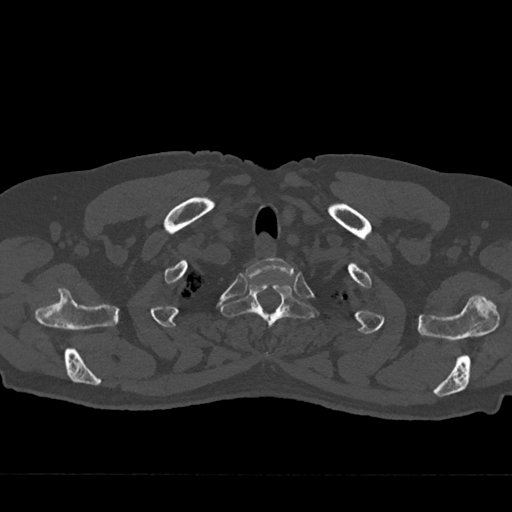
CT including the spine, one axial slice; slice 625 of 797 in the series (ordered by position); reconstruction kernel Br40s/3; 120 kVp; bone window (W 1800 / L 400 HU); 0.5 mm slice thickness; 512 × 512 image matrix. Male patient, age 75 years. Case-level facts recorded for this patient, not image findings: primary cancer: renal; vertebrae with lytic lesions (as recorded): T4.
Outlined on this slice (semi-automatic segmentation, software-assisted and operator-edited):
- T1 vertebra: bounding box (x1, y1, x2, y2) in pixels: (245, 258, 294, 279)
- T2 vertebra: (221, 284, 318, 356)